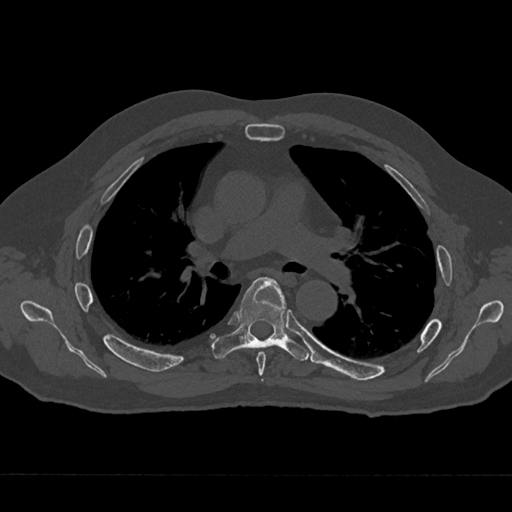
CT including the spine, one axial slice. Position 440 of 797 along the scan axis. Reconstruction kernel Br40s/3. 120 kVp. Bone window (W 1800 / L 400 HU). 0.5 mm slice thickness. 512 × 512 image matrix. Male patient, age 75 years. Case-level facts recorded for this patient, not image findings: primary cancer: renal.
Outlined on this slice (semi-automatic segmentation, software-assisted and operator-edited):
- T5 vertebra: bounding box <256,351,266,376> (left, top, right, bottom; pixels)
- T6 vertebra: <212,277,309,361>